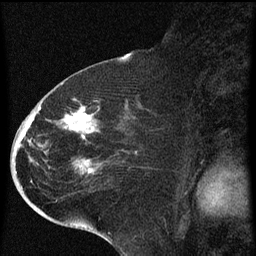
Breast MRI (dynamic contrast-enhanced), one sagittal slice; slice 32 of 60 in the series (ordered by position); dynamic contrast-enhanced series, image 2 of 4 at this slice position (ordered by acquisition); 1.5 T; TE 4.2 ms, TR 8 ms; 2 mm slice thickness; 256 × 256 image matrix. Patient: female, 71 years.
Outlined on this slice (semi-automatic segmentation, software-assisted and operator-edited):
- analysis volume of interest (the breast-tissue region the enhancement analysis was run in; not a lesion): bounding box <32,86,141,205> (left, top, right, bottom; pixels)
- tumour enhancement mask (voxels above the 70 % enhancement threshold inside the analysis volume of interest): <39,100,99,173>